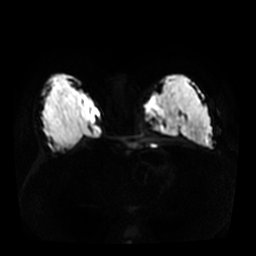
Breast MRI, one axial slice. Slice 18 of 36 in the series (ordered by position). Diffusion-weighted series; image 2 of 4 stored at this slice position (different b-values; order by instance number). 3 T. 5 mm slice thickness. 256 × 256 image matrix, field of view 340 × 340 mm. Female patient.
Structures marked on this image (expert manual segmentation):
- tumour on diffusion-weighted imaging: bounding box [x1, y1, x2, y2] px = [148, 94, 182, 136]